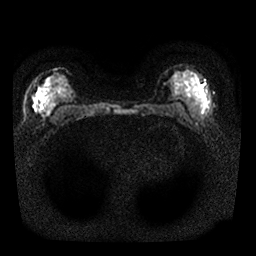
Breast MRI, one axial slice; position 13 of 25 along the scan axis; diffusion-weighted series; image 2 of 4 stored at this slice position (different b-values; order by instance number); 1.5 T; 4 mm slice thickness; 256 × 256 image matrix, field of view 310 × 310 mm. Female patient.
Outlined on this slice (manually delineated by an expert):
- tumour on diffusion-weighted imaging: box from (x=39, y=94) to (x=42, y=98) px